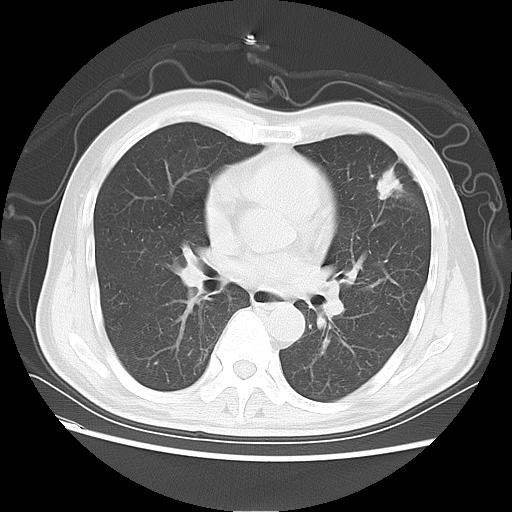
Chest CT, one axial slice; position 33 of 64 along the scan axis; reconstruction kernel LUNG; lung window (W 1500 / L -600 HU); 5 mm slice thickness; 512 × 512 image matrix. Patient: male, 60 years. From the clinical record (not read from this slice): clinical TNM (as recorded): T2a N0 M0; histopathological grade: G3.
Annotated regions visible in this slice (rectangle marked by the reading radiologist):
- lung tumour (recorded histology: adenocarcinoma): bounding box (x1, y1, x2, y2) in pixels: (370, 154, 403, 212)